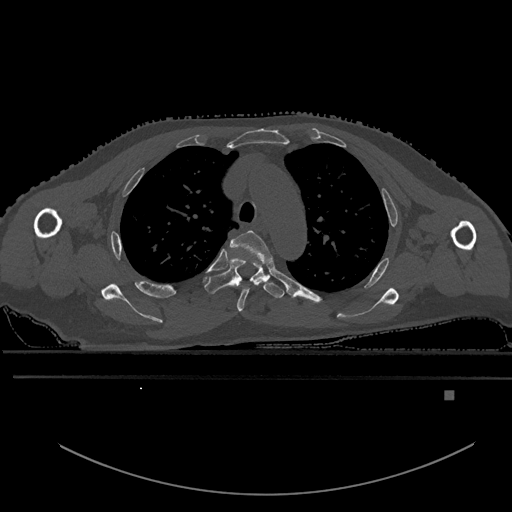
CT including the spine, one axial slice; slice 424 of 969 in the series (ordered by position); bone window (W 1800 / L 400 HU); 0.5 mm slice thickness; 512 × 512 image matrix, field of view 456 × 456 mm. Patient: male, 82 years. Case-level facts recorded for this patient, not image findings: primary cancer: prostate; vertebrae with lytic lesions (as recorded): T11, T9, T8, T2.
Structures marked on this image (semi-automatic segmentation, software-assisted and operator-edited):
- T3 vertebra: bounding box (x1, y1, x2, y2) in pixels: (231, 230, 273, 312)
- T4 vertebra: (204, 257, 285, 299)